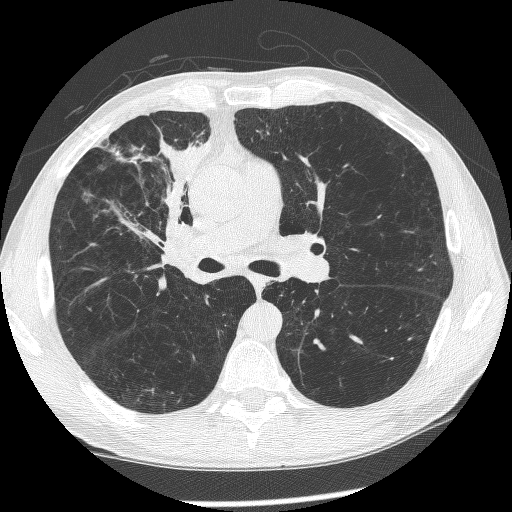
Axial slice from a low-dose chest CT screening exam; baseline screening round; lung window (W 1500 / L -600 HU); lung (sharp) reconstruction kernel (BONE); slice 143 of 266 in the series. Male participant, aged 60 years at enrolment.
• Expert reader's lesion annotation, bounding box (x1, y1, x2, y2) in pixels: (145, 187, 219, 280).
• The exam's reader record, not a measurement of the box and not confirmed to be the same lesion: non-calcified nodule or mass ≥4 mm, right upper lobe, 12 × 8 mm, spiculated (stellate) margins, mixed attenuation.
• Official screen result: positive, change unspecified: nodule(s) >= 4 mm or enlarging nodule(s), mass(es), or other non-specific abnormalities suspicious for lung cancer.
• Lung cancer was diagnosed 208 days after this screen: squamous cell carcinoma, NOS, right upper lobe, right middle lobe, right main stem bronchus, poorly differentiated (G3), stage IV (AJCC 6th edition).